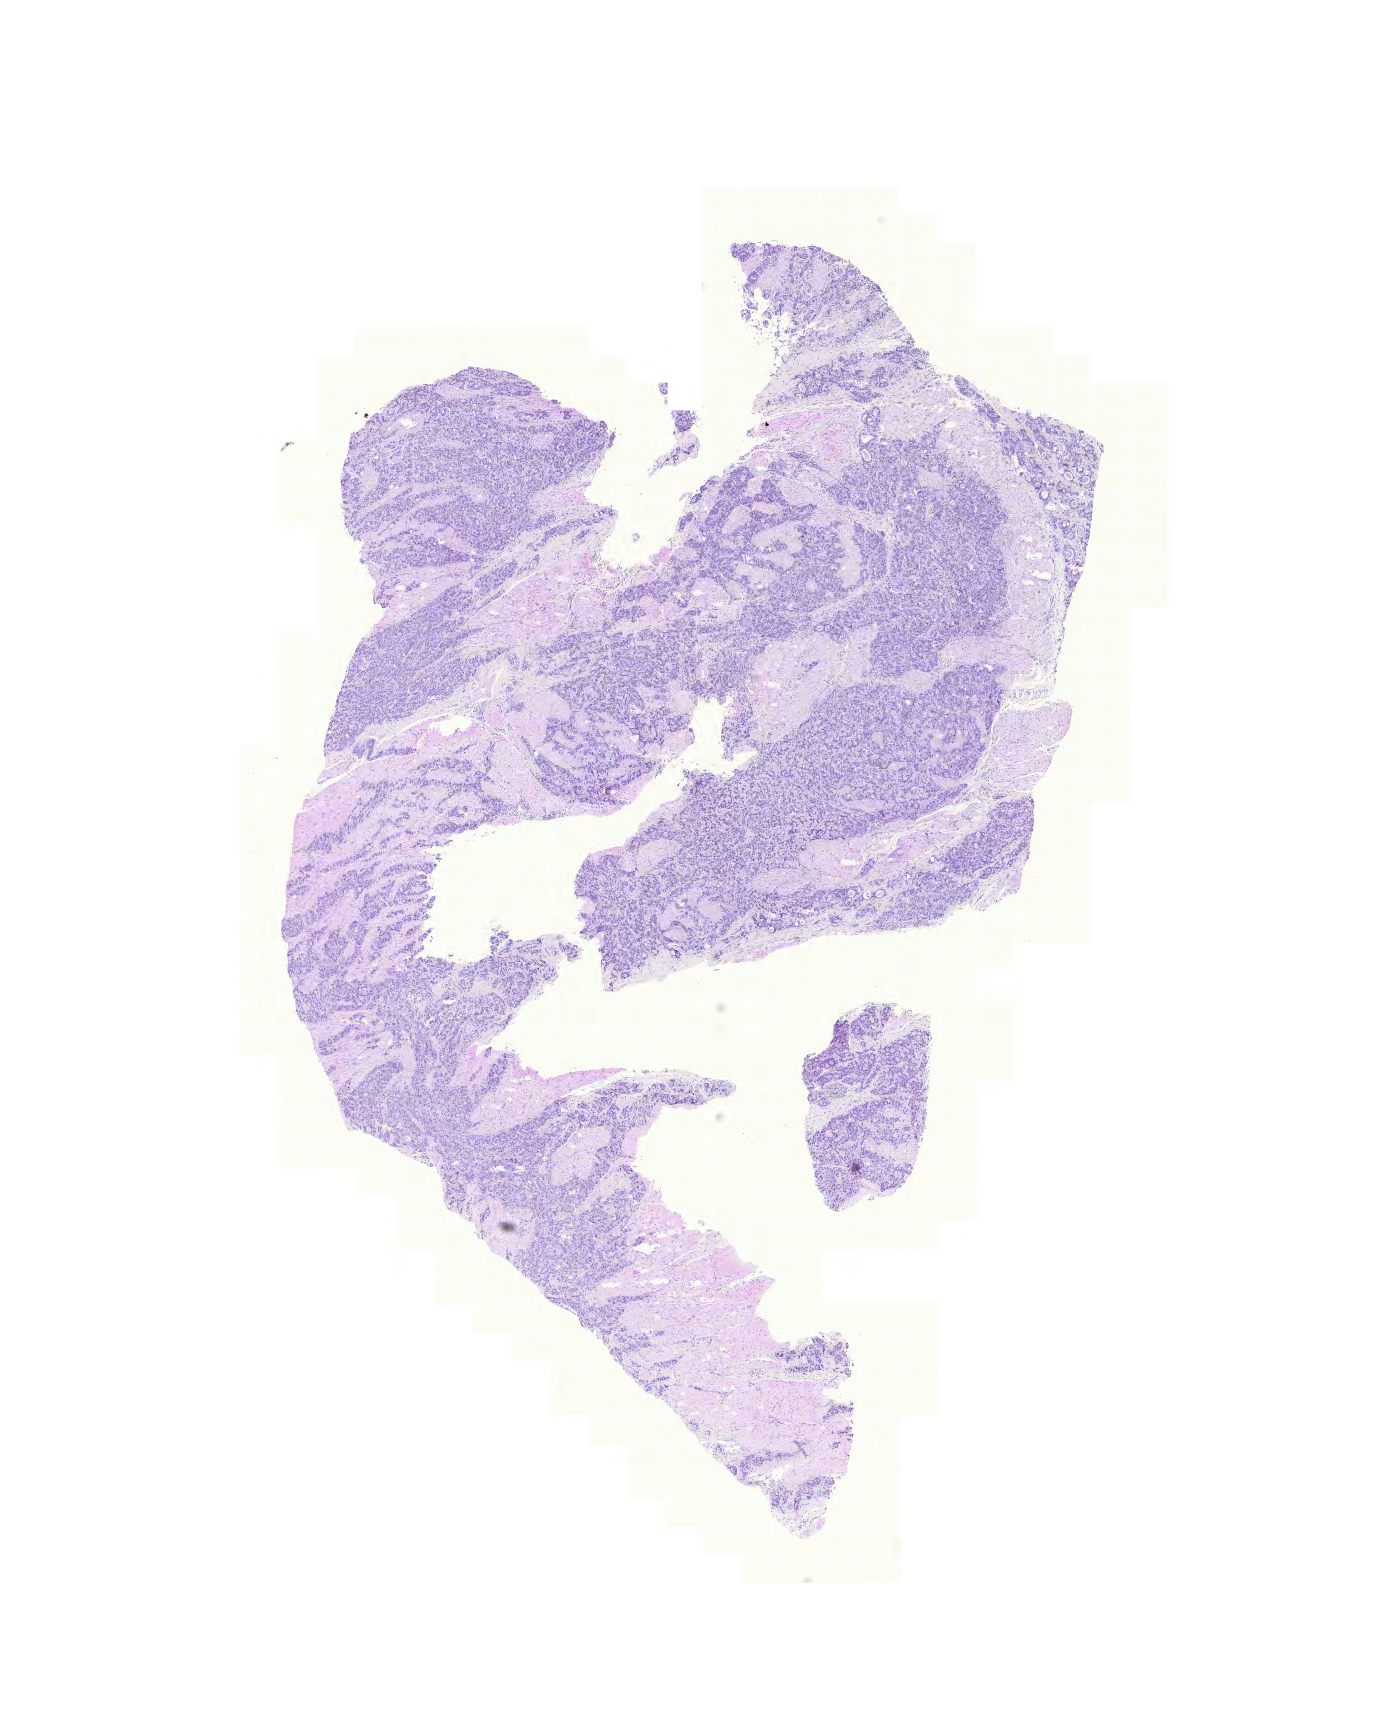
H&E-stained whole-slide image, a low-resolution overview of the entire scanned area, about 10.3 x 12.9 mm (acquisition: 20x scan). Formalin-fixed paraffin-embedded (FFPE) diagnostic section. Stomach, primary tumour sample. Patient: male, age at initial diagnosis 49 years. Histologic grade: G3 (poorly differentiated).
• diagnosis: Adenocarcinoma with mixed subtypes (gastric antrum)
• AJCC pathologic stage: IV (6th edition)